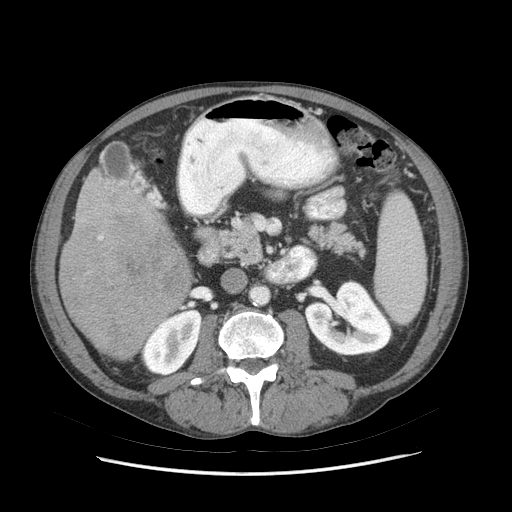
Contrast-enhanced abdominal CT (liver protocol), one axial slice; slice 26 of 89 in the series (ordered by position); reconstruction kernel STANDARD; 140 kVp; soft-tissue window (W 400 / L 40 HU); 2.5 mm slice thickness; 512 × 512 image matrix. Case-level facts recorded for this patient, not image findings: diagnosis: hepatocellular carcinoma (patient treated with transarterial chemoembolisation; whether this scan precedes or follows treatment is not stated here); TNM stage (as recorded): Stage-IIIB; Child-Pugh class: A; tumour differentiation: moderately differentiated; tumour nodularity: multinodular.
Structures marked on this image (semi-automatic segmentation, software-assisted and operator-edited):
- liver parenchyma outside the tumour (the mass and vessels are separate outlines, so this box may not span the whole liver): bounding box (x1, y1, x2, y2) in pixels: (58, 169, 172, 360)
- mass: (58, 202, 192, 358)